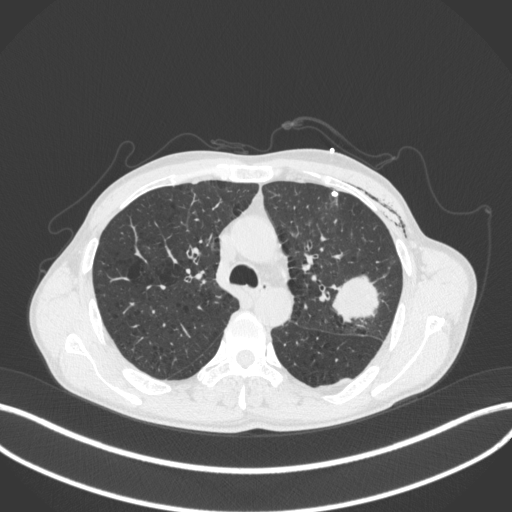
Chest CT, one axial slice; slice 273 of 416 in the series (ordered by position); 120 kVp; lung window (W 1500 / L -600 HU); 512 × 512 image matrix, field of view 400 × 400 mm. Male patient, age 58 years. From the clinical record (not read from this slice): clinical TNM (as recorded): T3 N0 M0.
Annotated regions visible in this slice (bounding box drawn by a radiologist):
- lung tumour (recorded histology: adenocarcinoma): bounding box <329,273,381,328> (left, top, right, bottom; pixels)